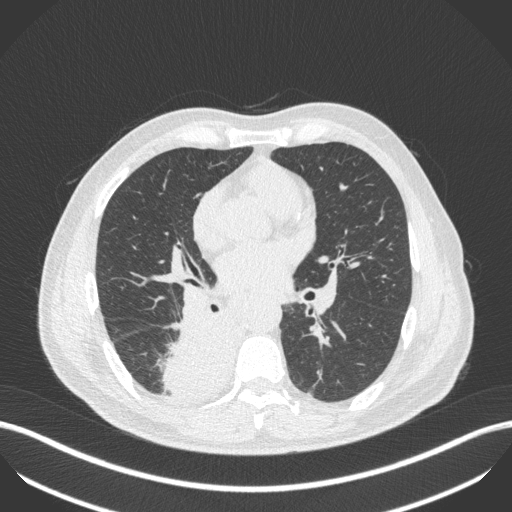
Chest CT, one axial slice. Position 241 of 451 along the scan axis. Lung window (W 1500 / L -600 HU). 1 mm slice thickness. 512 × 512 image matrix. Patient: male, 61 years. From the clinical record (not read from this slice): clinical TNM (as recorded): T1 N0 M0.
Outlined on this slice (bounding box drawn by a radiologist):
- lung tumour (recorded histology: small cell carcinoma): bounding box <156,314,229,402> (left, top, right, bottom; pixels)